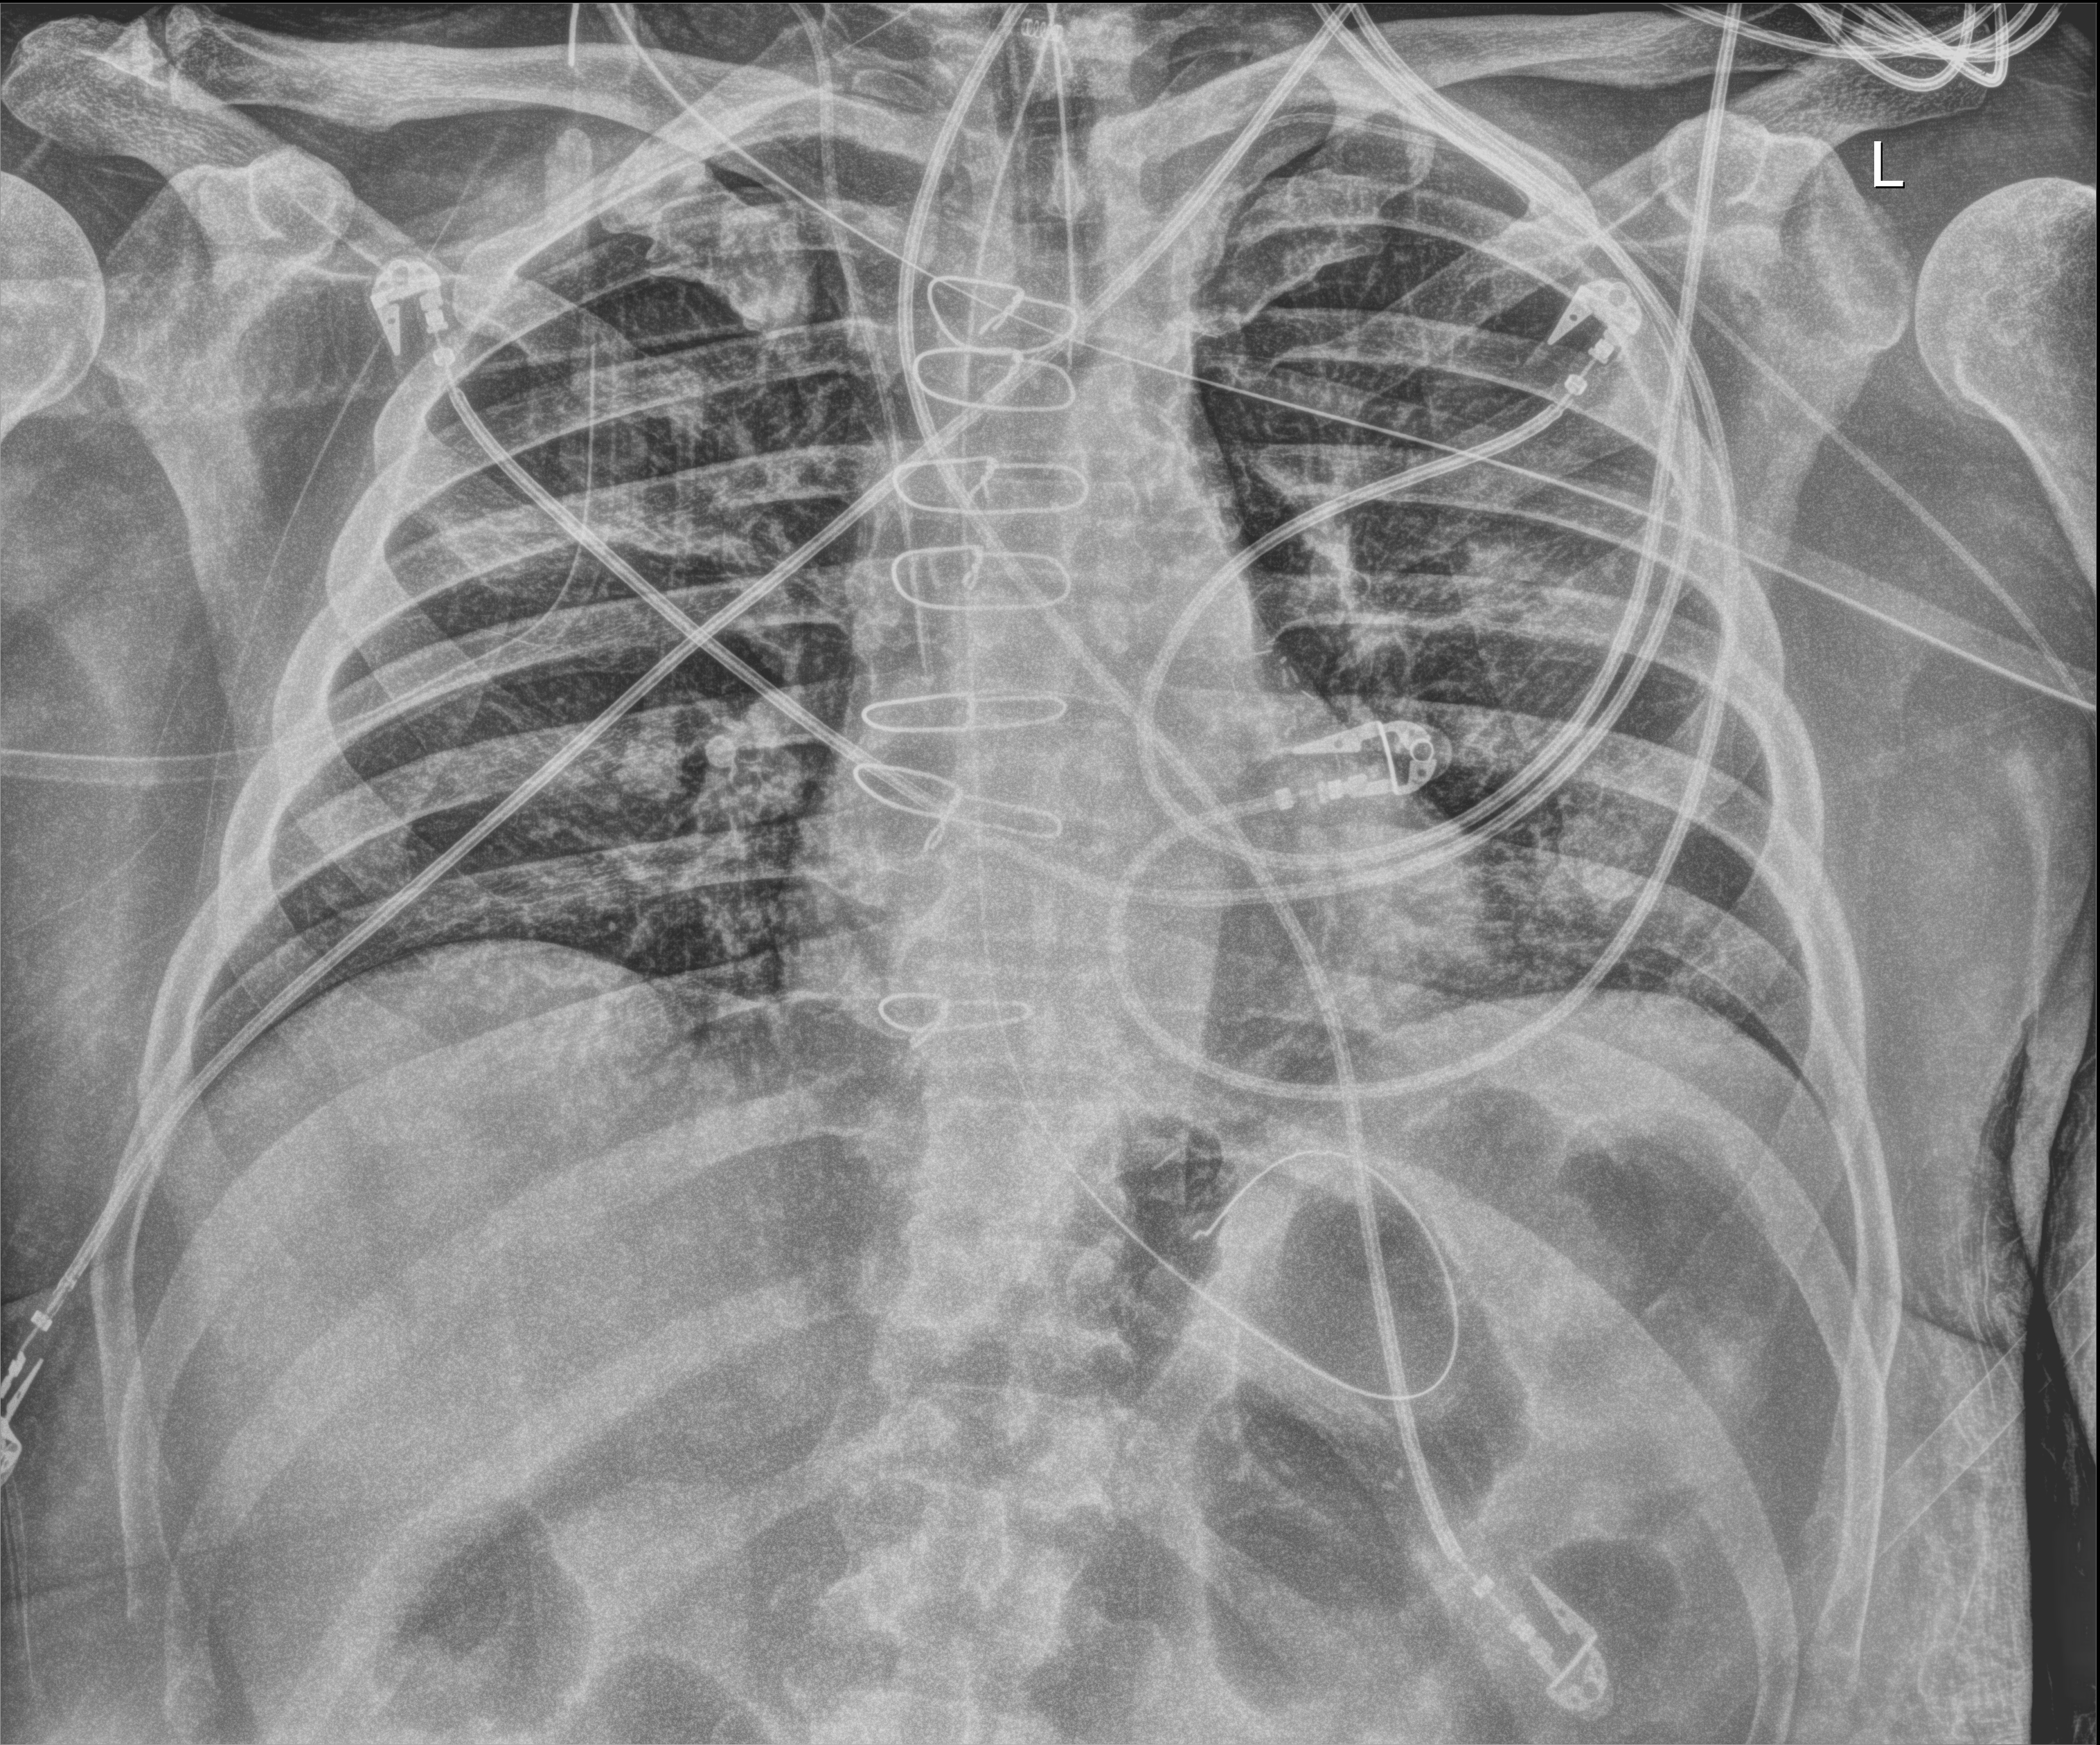
Bedside chest radiograph (digital radiography), anteroposterior (AP) projection. Male patient hospitalised with COVID-19, age 60–74 years.
Hospital-stay facts (about this admission, not read from this image; timing relative to this image not recorded):
- COPD (admission record): no
- hypertension (admission record): yes